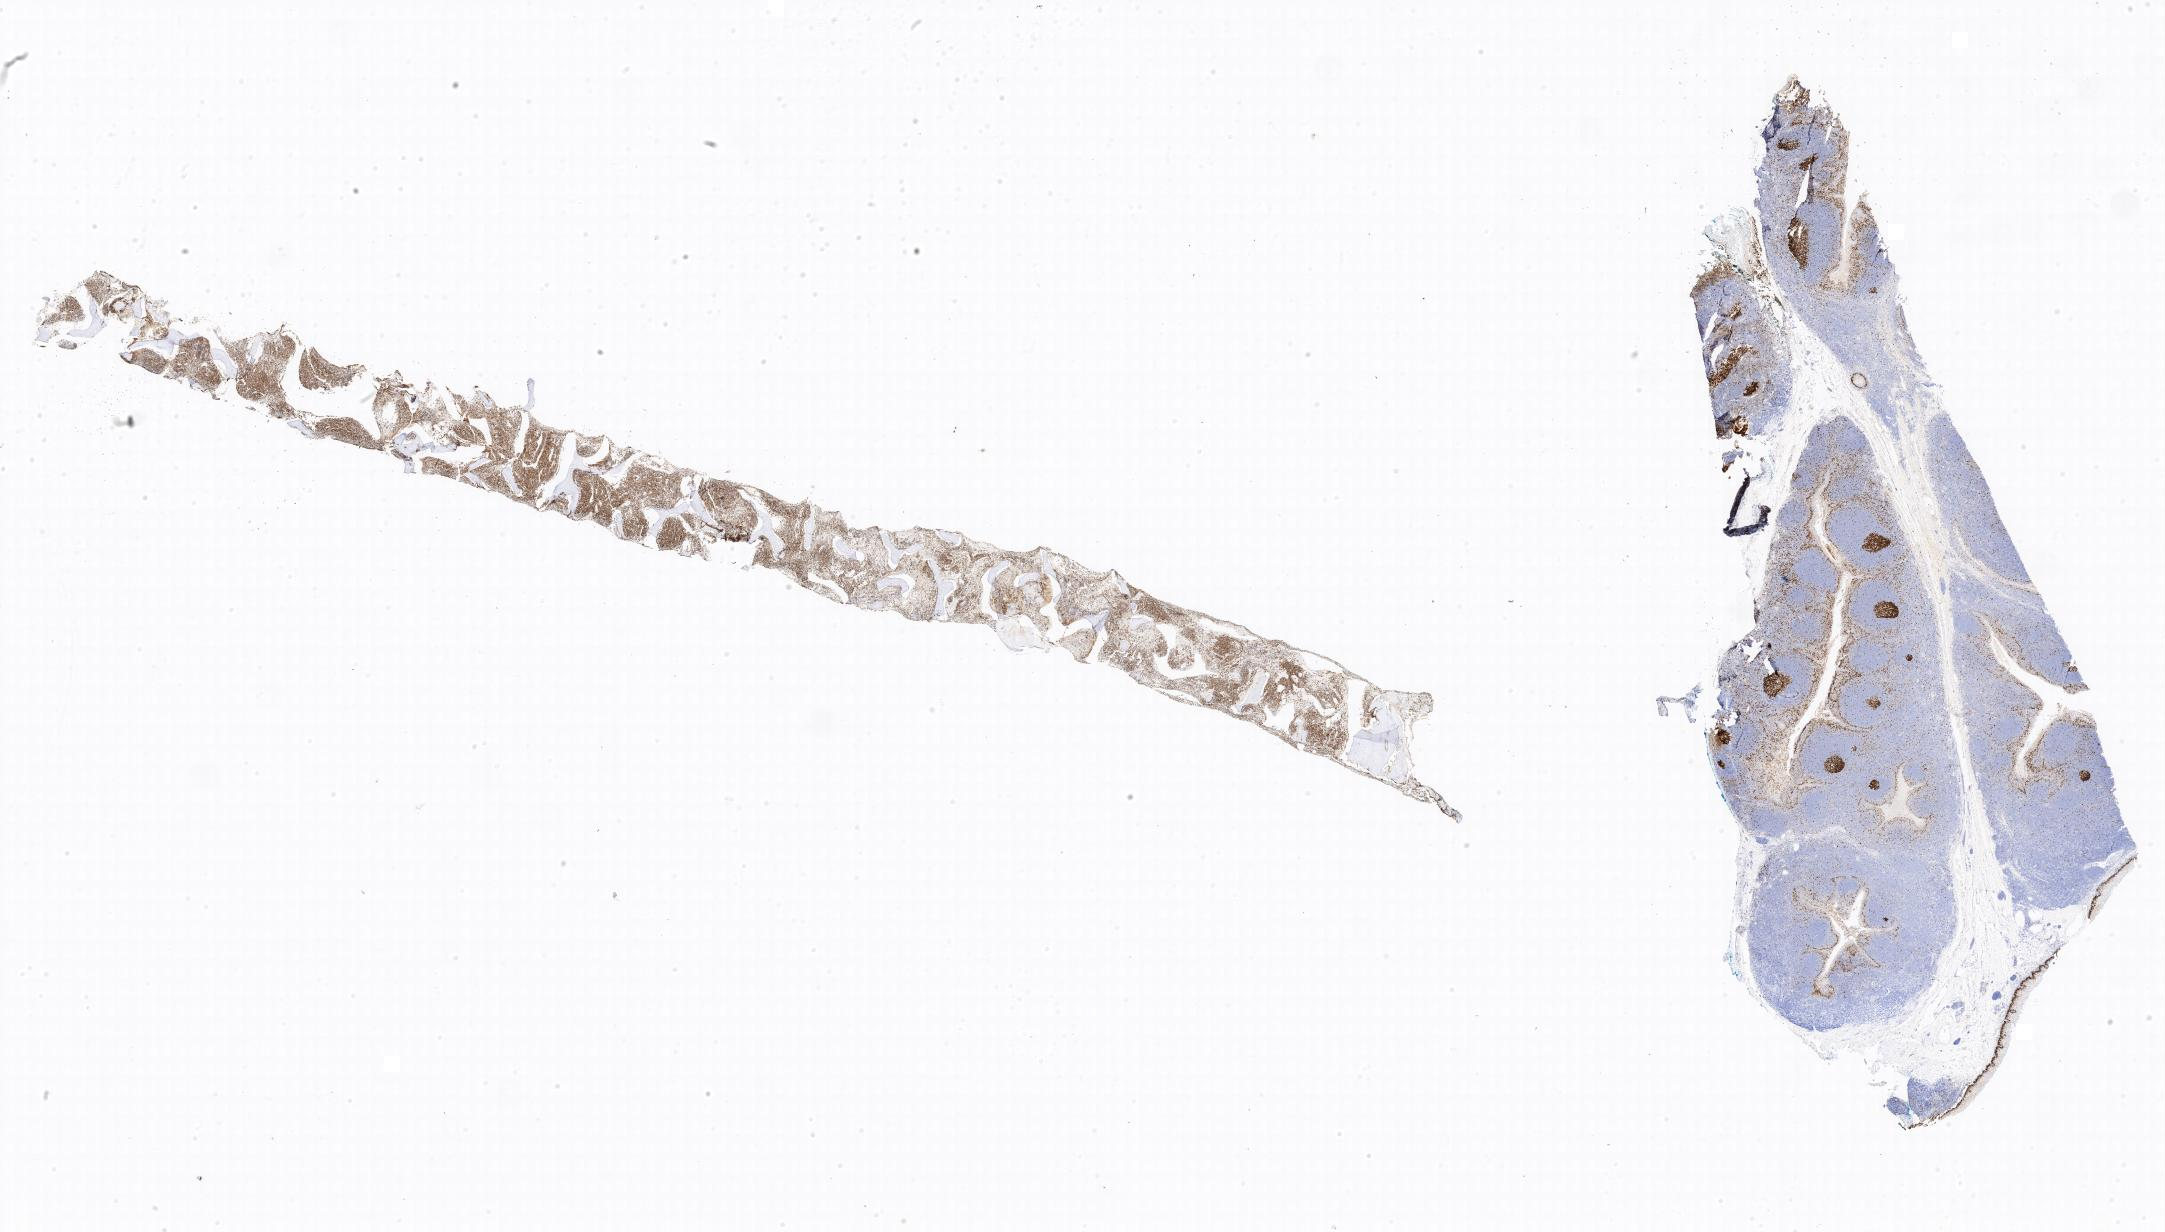
Whole-slide image, immunohistochemical stain for Ki-67, whole scanned area shown as a low-resolution overview. Specimen: tumor tissue. Site: bone marrow. Patient: male, age 18 years.
Diagnosis: Burkitt lymphoma, NOS.